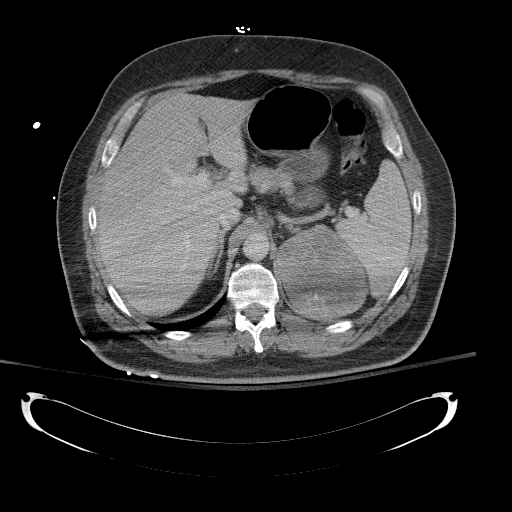
Contrast-enhanced abdominal CT, one axial slice. Position 91 of 154 along the scan axis. Reconstruction kernel B41f. 120 kVp. Intravenous contrast given. Soft-tissue window (W 400 / L 40 HU). 512 × 512 image matrix, field of view 467 × 467 mm. Male patient, age 43 years. Case-level facts recorded for this patient, not image findings: diagnosis: adrenocortical carcinoma; tumour side: left adrenal; tumour size at pathology: 9.8 cm; Ki-67 index: 30 %; stage (as recorded): 2.
Annotated regions visible in this slice (semi-automatically segmented with operator editing):
- mass: bounding box (x1, y1, x2, y2) in pixels: (279, 226, 363, 317)